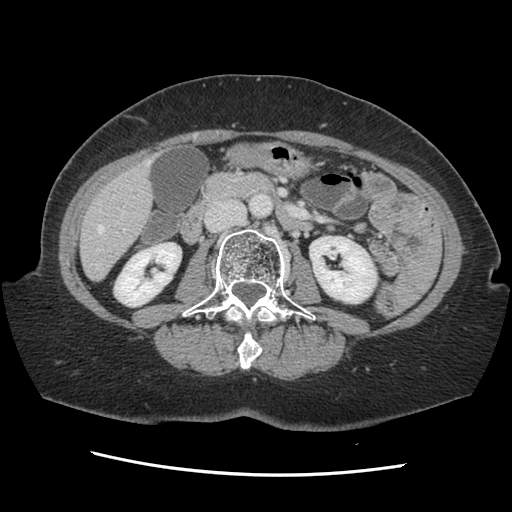
Contrast-enhanced abdominal CT, one axial slice; slice 46 of 141 in the series (ordered by position); soft-tissue window (W 400 / L 40 HU); 2.5 mm slice thickness; 512 × 512 image matrix, field of view 330 × 330 mm. Female patient, age 61 years. Case-level facts recorded for this patient, not image findings: diagnosis: colorectal cancer liver metastases, imaged before liver resection; multiple liver metastases: no; largest metastasis: 2.4 cm.
Structures marked on this image (expert manual segmentation):
- hepatic veins: box from (x=96, y=161) to (x=149, y=269) px
- liver: (x=82, y=164)–(x=153, y=279)
- planned liver remnant (the part of the liver to remain after resection): (x=82, y=183)–(x=153, y=279)
- portal vein (with intrahepatic branches): (x=98, y=230)–(x=125, y=250)